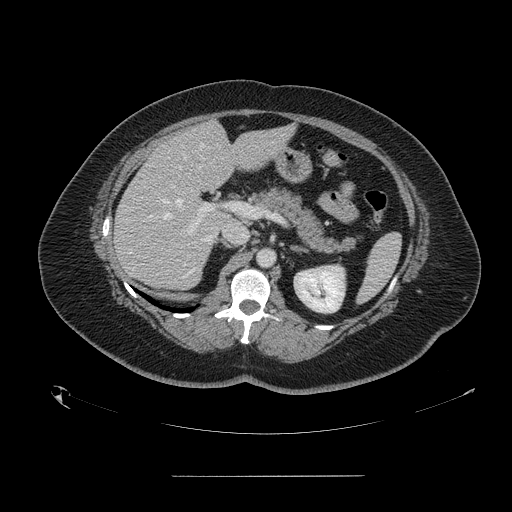
Contrast-enhanced abdominal CT, one axial slice; slice 86 of 164 in the series (ordered by position); 120 kVp; intravenous contrast given; soft-tissue window (W 400 / L 40 HU); 512 × 512 image matrix, field of view 495 × 495 mm. Female patient, age 52 years. From the clinical record (not read from this slice): diagnosis: colorectal cancer liver metastases, imaged before liver resection; multiple liver metastases: yes; largest metastasis: 3.5 cm.
Annotated regions visible in this slice (expert manual segmentation):
- hepatic veins: box from (x=161, y=143) to (x=203, y=219) px
- liver: (x=114, y=121)–(x=291, y=289)
- planned liver remnant (the part of the liver to remain after resection): (x=177, y=122)–(x=290, y=219)
- portal vein (with intrahepatic branches): (x=171, y=185)–(x=212, y=234)